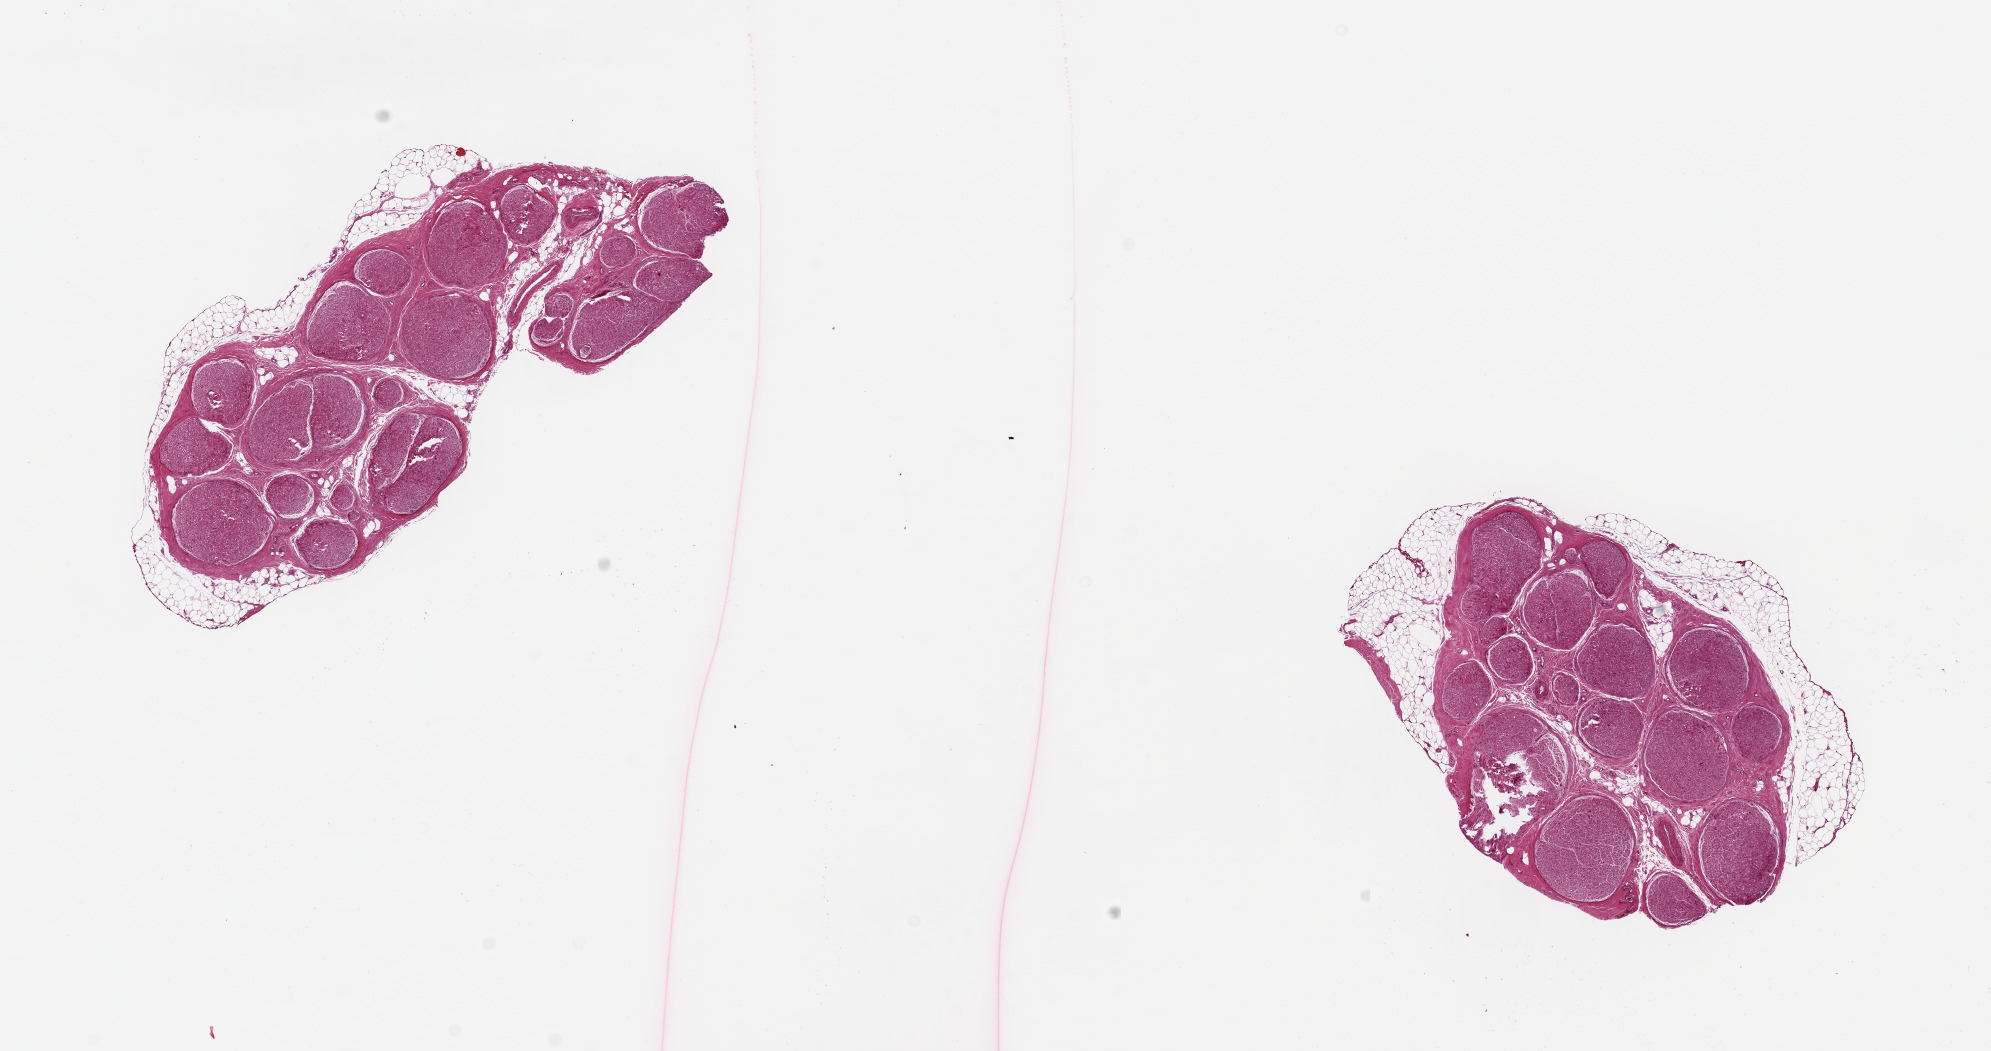
H&E whole-slide image, whole scanned area (about 15.8 x 8.3 mm) shown as a low-resolution overview. PAXgene-fixed paraffin-embedded (PFPE) section. Section of tibial nerve (target tissue). Donor tissue sample. Donor: female.
- reviewer comment on this tissue sample: 2 pieces. 5x2 & 4x3mm; 20% external adipose